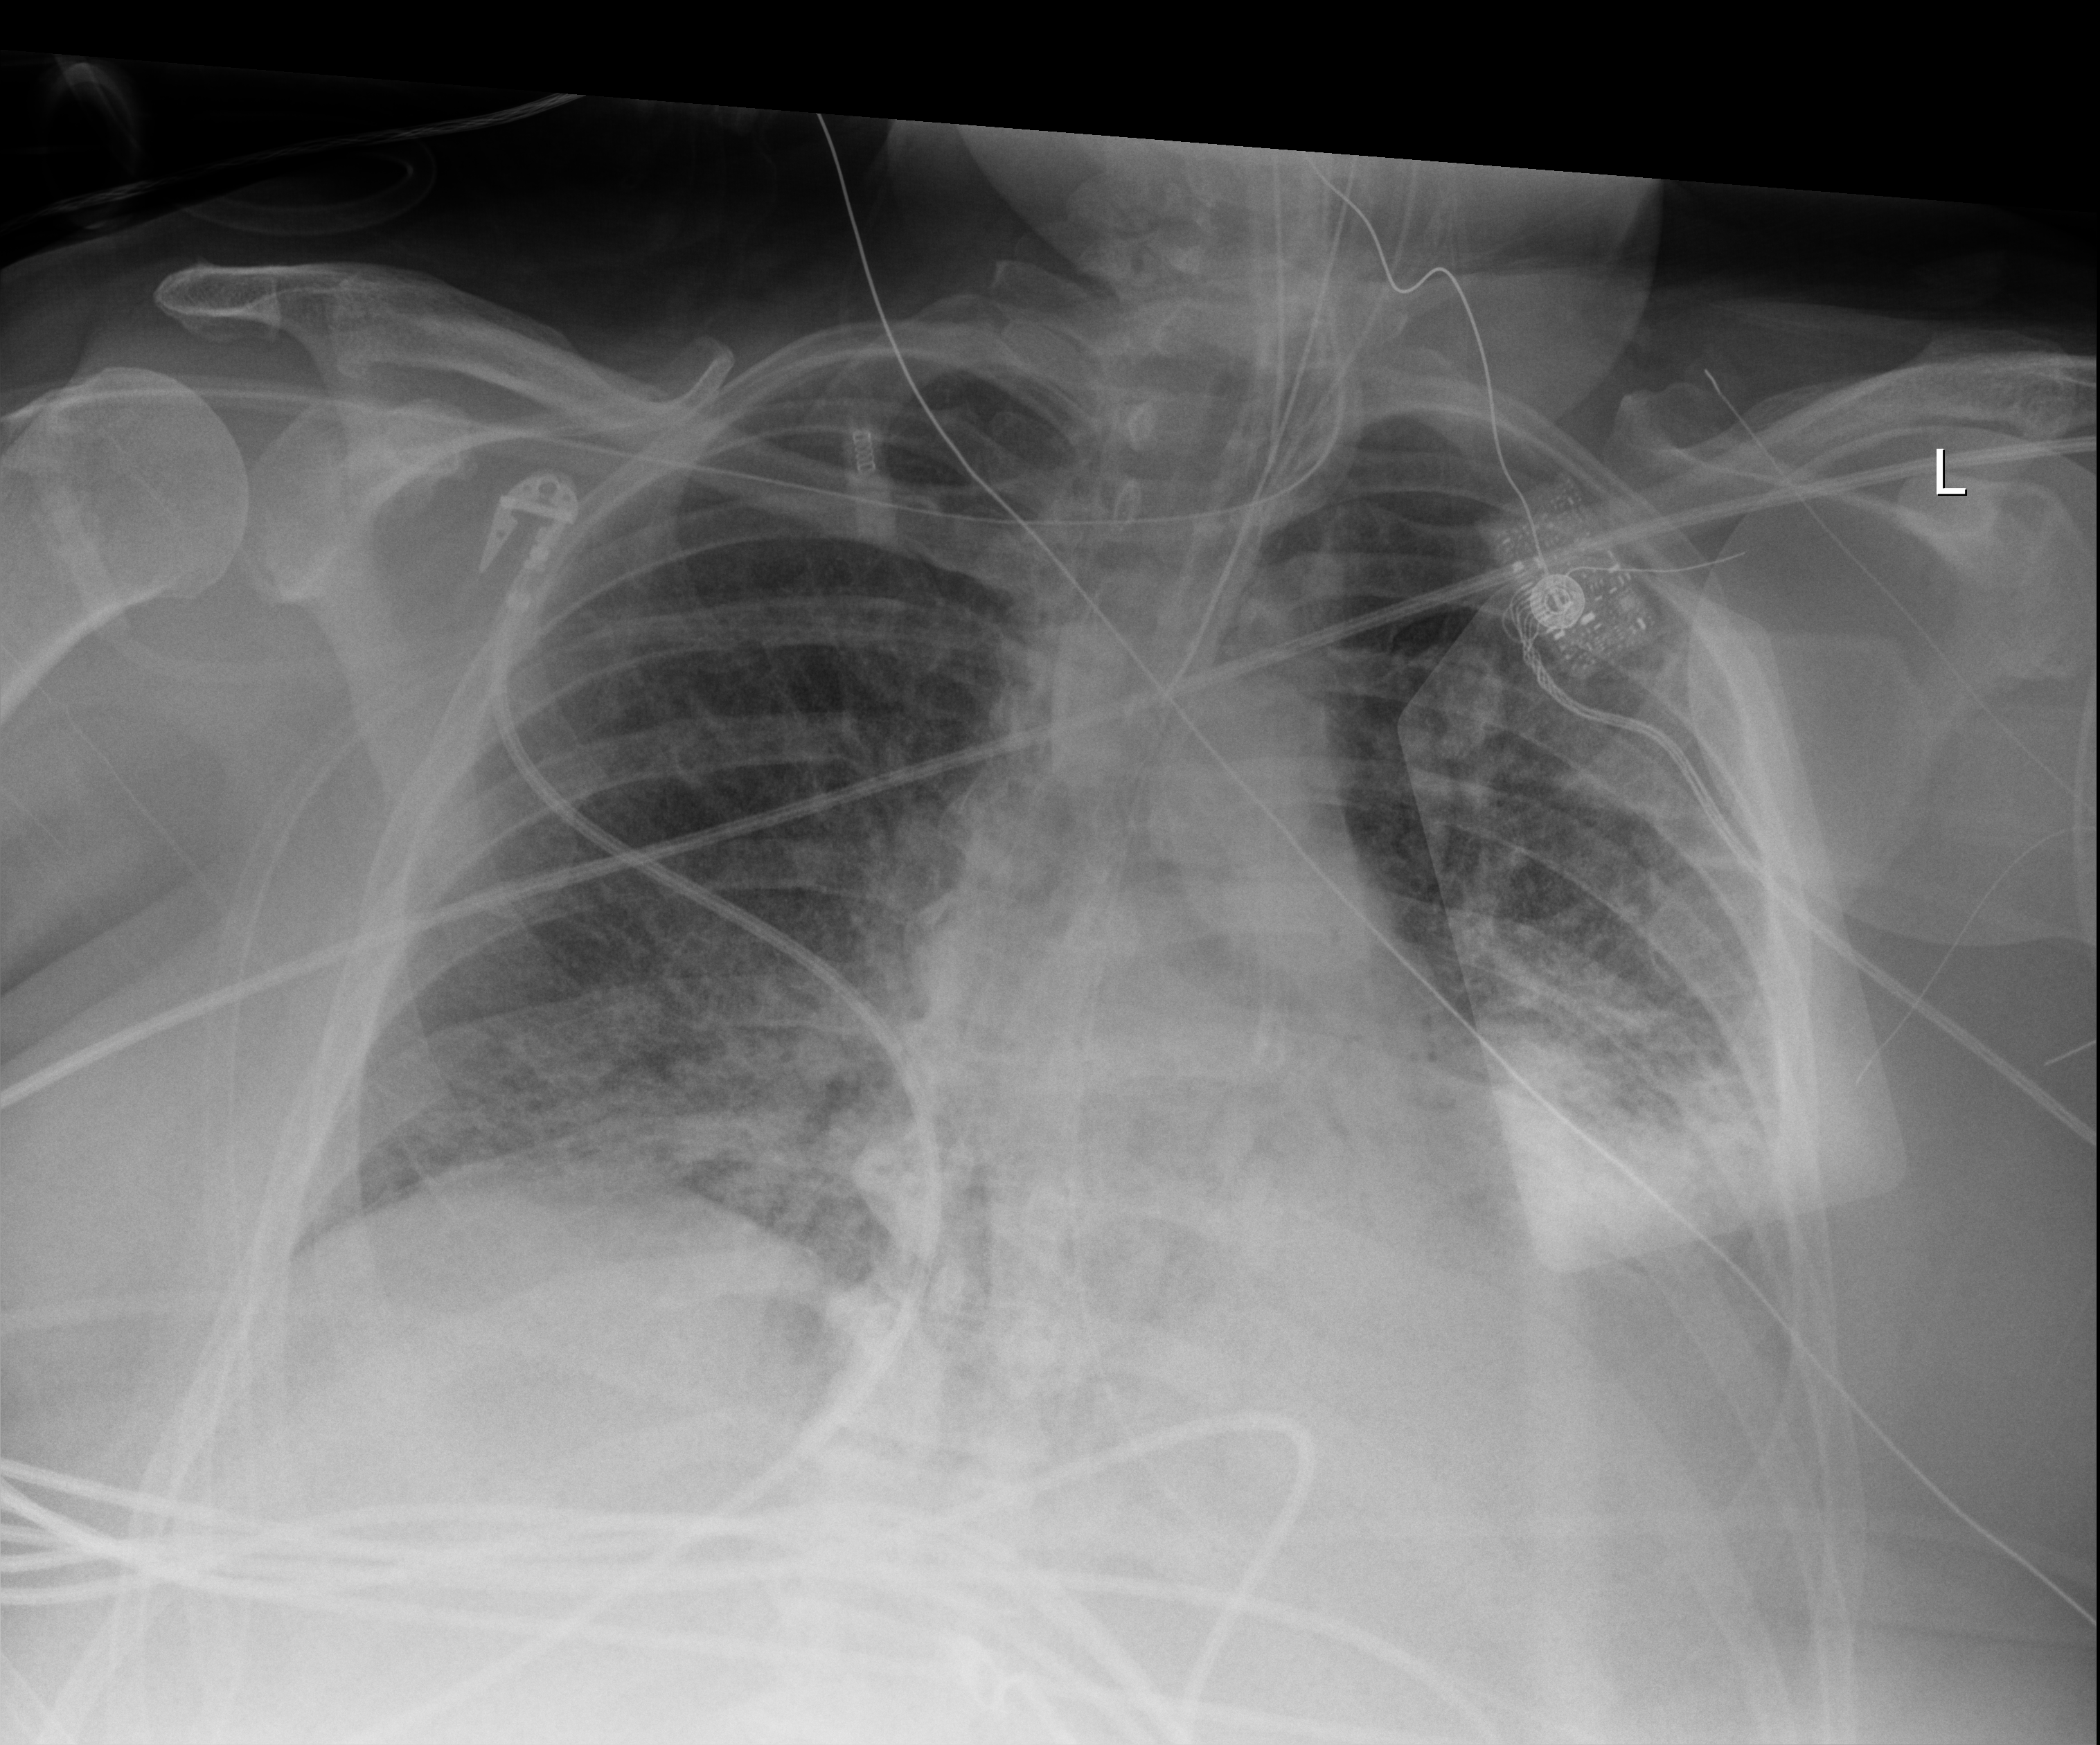
Bedside chest radiograph (digital radiography); anteroposterior (AP) projection. Patient hospitalised with COVID-19, aged 18–59 years.
Hospital-stay facts (about this admission, not read from this image; timing relative to this image not recorded): mechanically ventilated during this hospital stay: yes.